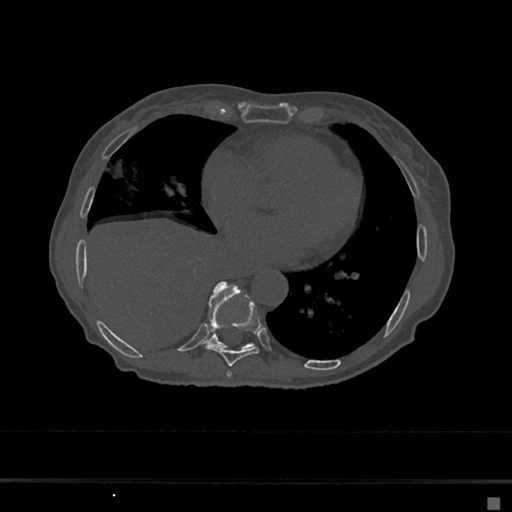
CT including the spine, one axial slice. Position 306 of 797 along the scan axis. Reconstruction kernel Br40s/3. Bone window (W 1800 / L 400 HU). 0.5 mm slice thickness. 512 × 512 image matrix, field of view 360 × 360 mm. Female patient, age 68 years. From the clinical record (not read from this slice): primary cancer: renal.
Annotated regions visible in this slice (semi-automatic segmentation, software-assisted and operator-edited):
- T7 vertebra: bounding box (x1, y1, x2, y2) in pixels: (226, 371, 232, 378)
- T8 vertebra: (205, 299, 261, 367)
- T9 vertebra: (207, 281, 253, 349)